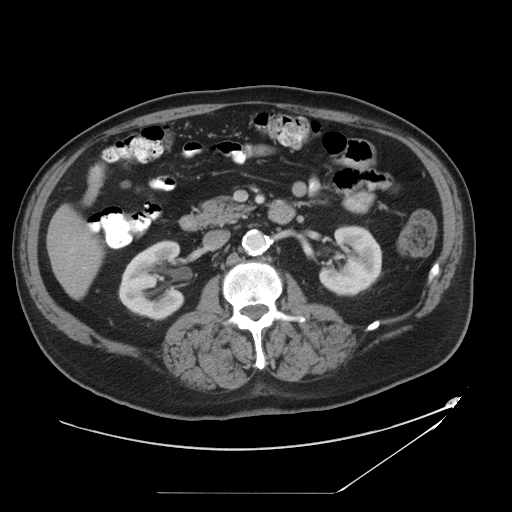
Contrast-enhanced abdominal CT, one axial slice. Slice 15 of 49 in the series (ordered by position). Reconstruction kernel STANDARD. 120 kVp. Intravenous contrast given. Soft-tissue window (W 400 / L 40 HU). 5 mm slice thickness. 512 × 512 image matrix. Male patient, age 72 years. From the clinical record (not read from this slice): diagnosis: colorectal cancer liver metastases, imaged before liver resection; multiple liver metastases: no; largest metastasis: 2.5 cm; chemotherapy before resection: yes.
Annotated regions visible in this slice (outlined manually by an expert reader):
- liver: bounding box [x1, y1, x2, y2] px = [49, 208, 102, 297]
- planned liver remnant (the part of the liver to remain after resection): [49, 208, 102, 297]